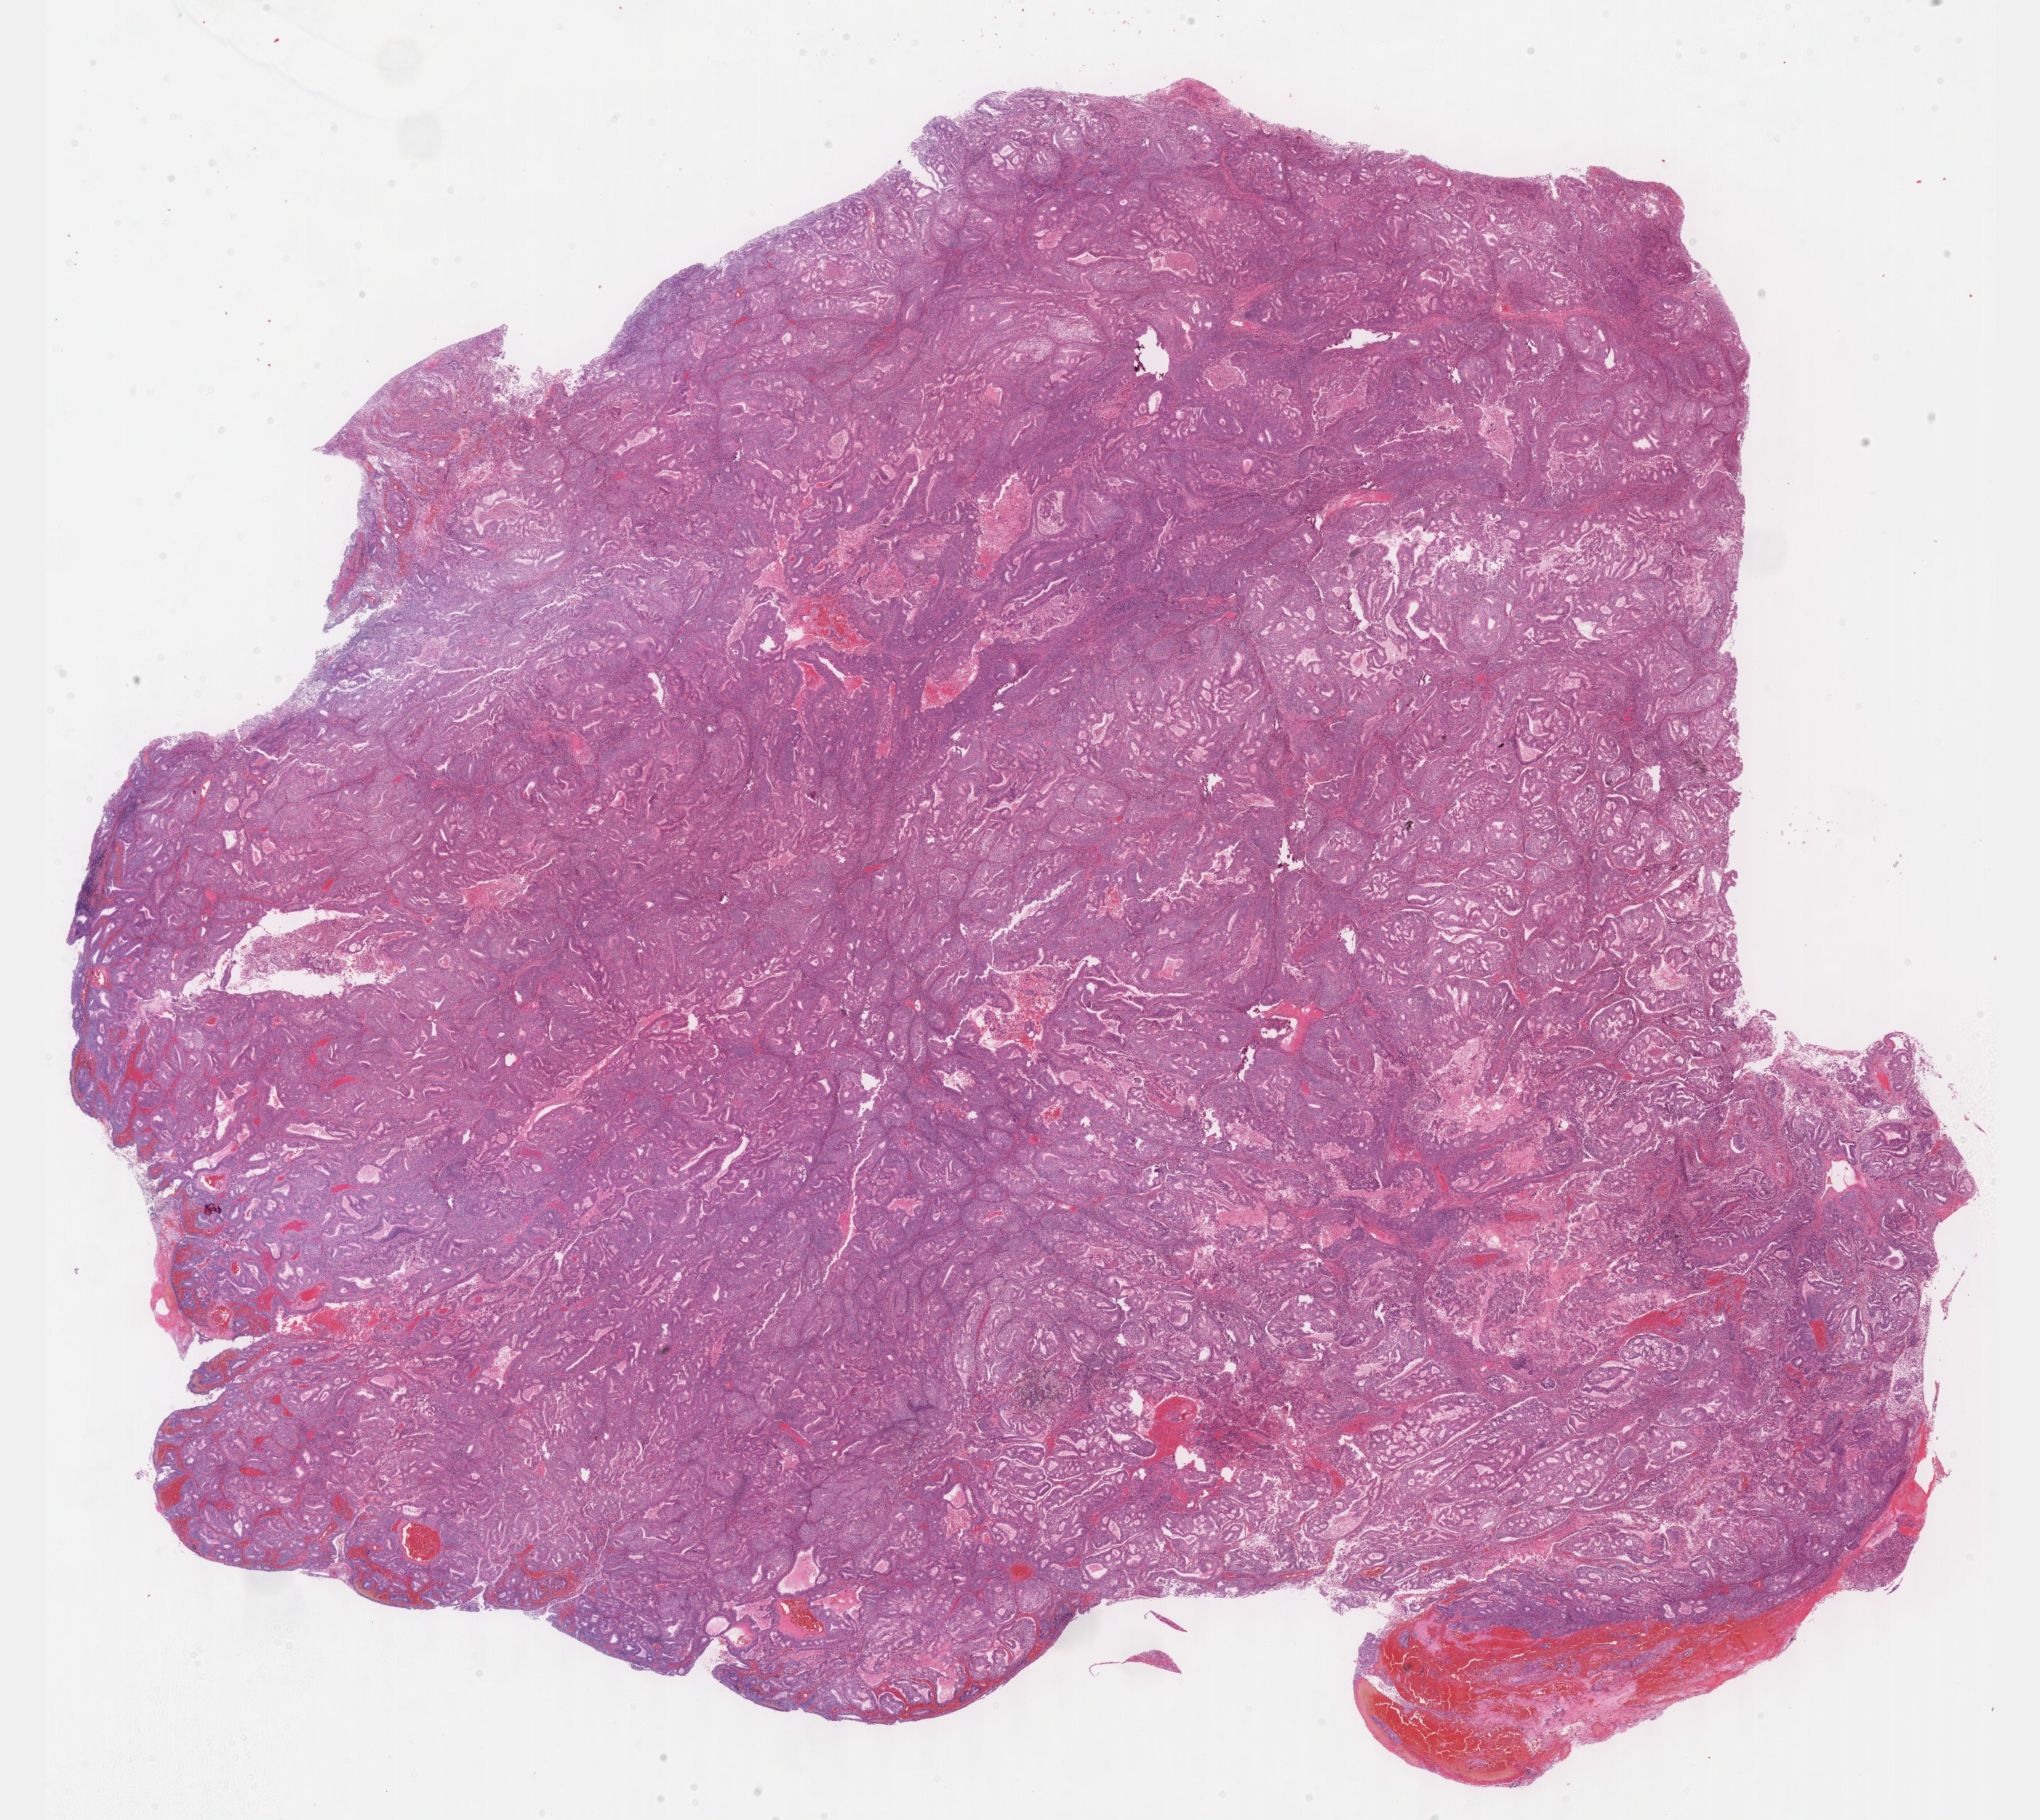
Hematoxylin and eosin (H&E) stained whole-slide image — whole scanned area (about 22.6 x 20.2 mm) shown as a low-resolution overview; formalin-fixed paraffin-embedded (FFPE) diagnostic section; sample: primary tumour, uterus. Female, age 70 years at initial diagnosis. Histologic grade: G2 (moderately differentiated).
• histologic diagnosis: Endometrioid adenocarcinoma, NOS (endometrium)
• FIGO stage: I